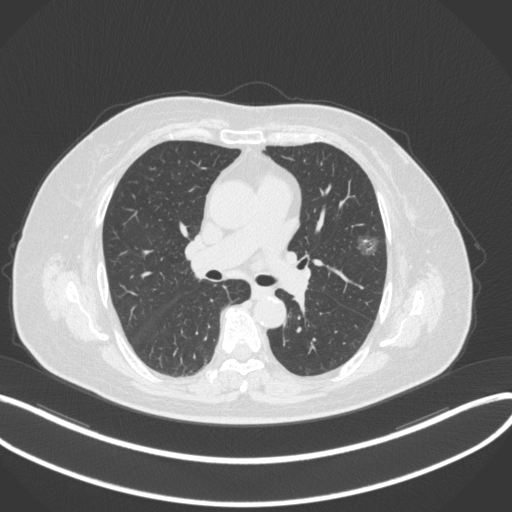
Chest CT, one axial slice; slice 181 of 286 in the series (ordered by position); reconstruction kernel B31f; lung window (W 1500 / L -600 HU); 512 × 512 image matrix. Female patient, age 76 years. From the clinical record (not read from this slice): clinical TNM (as recorded): T1b N0 M0; histopathological grade: G1-2.
Structures marked on this image (bounding box drawn by a radiologist):
- lung tumour (recorded histology: adenocarcinoma): bounding box [x1, y1, x2, y2] px = [353, 230, 384, 263]